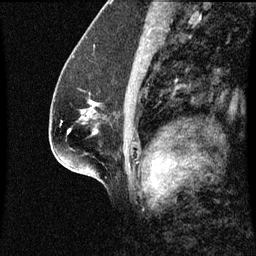
Breast MRI (dynamic contrast-enhanced), one sagittal slice. Slice 34 of 60 in the series (ordered by position). Dynamic contrast-enhanced series, image 2 of 3 at this slice position (ordered by acquisition). 1.5 T. TE 4.2 ms, TR 8.9 ms. 2 mm slice thickness. 256 × 256 image matrix, field of view 200 × 200 mm. Patient: female, 57 years. Case-level facts recorded for this patient, not image findings: setting: breast cancer imaged before/during neoadjuvant chemotherapy; receptor status: HR-positive, HER2-negative.
Annotated regions visible in this slice (semi-automatically segmented with operator editing):
- analysis volume of interest (the breast-tissue region the enhancement analysis was run in; not a lesion): bounding box (x1, y1, x2, y2) in pixels: (82, 92, 121, 125)
- tumour enhancement mask (voxels above the 70 % enhancement threshold inside the analysis volume of interest): (88, 112, 91, 115)